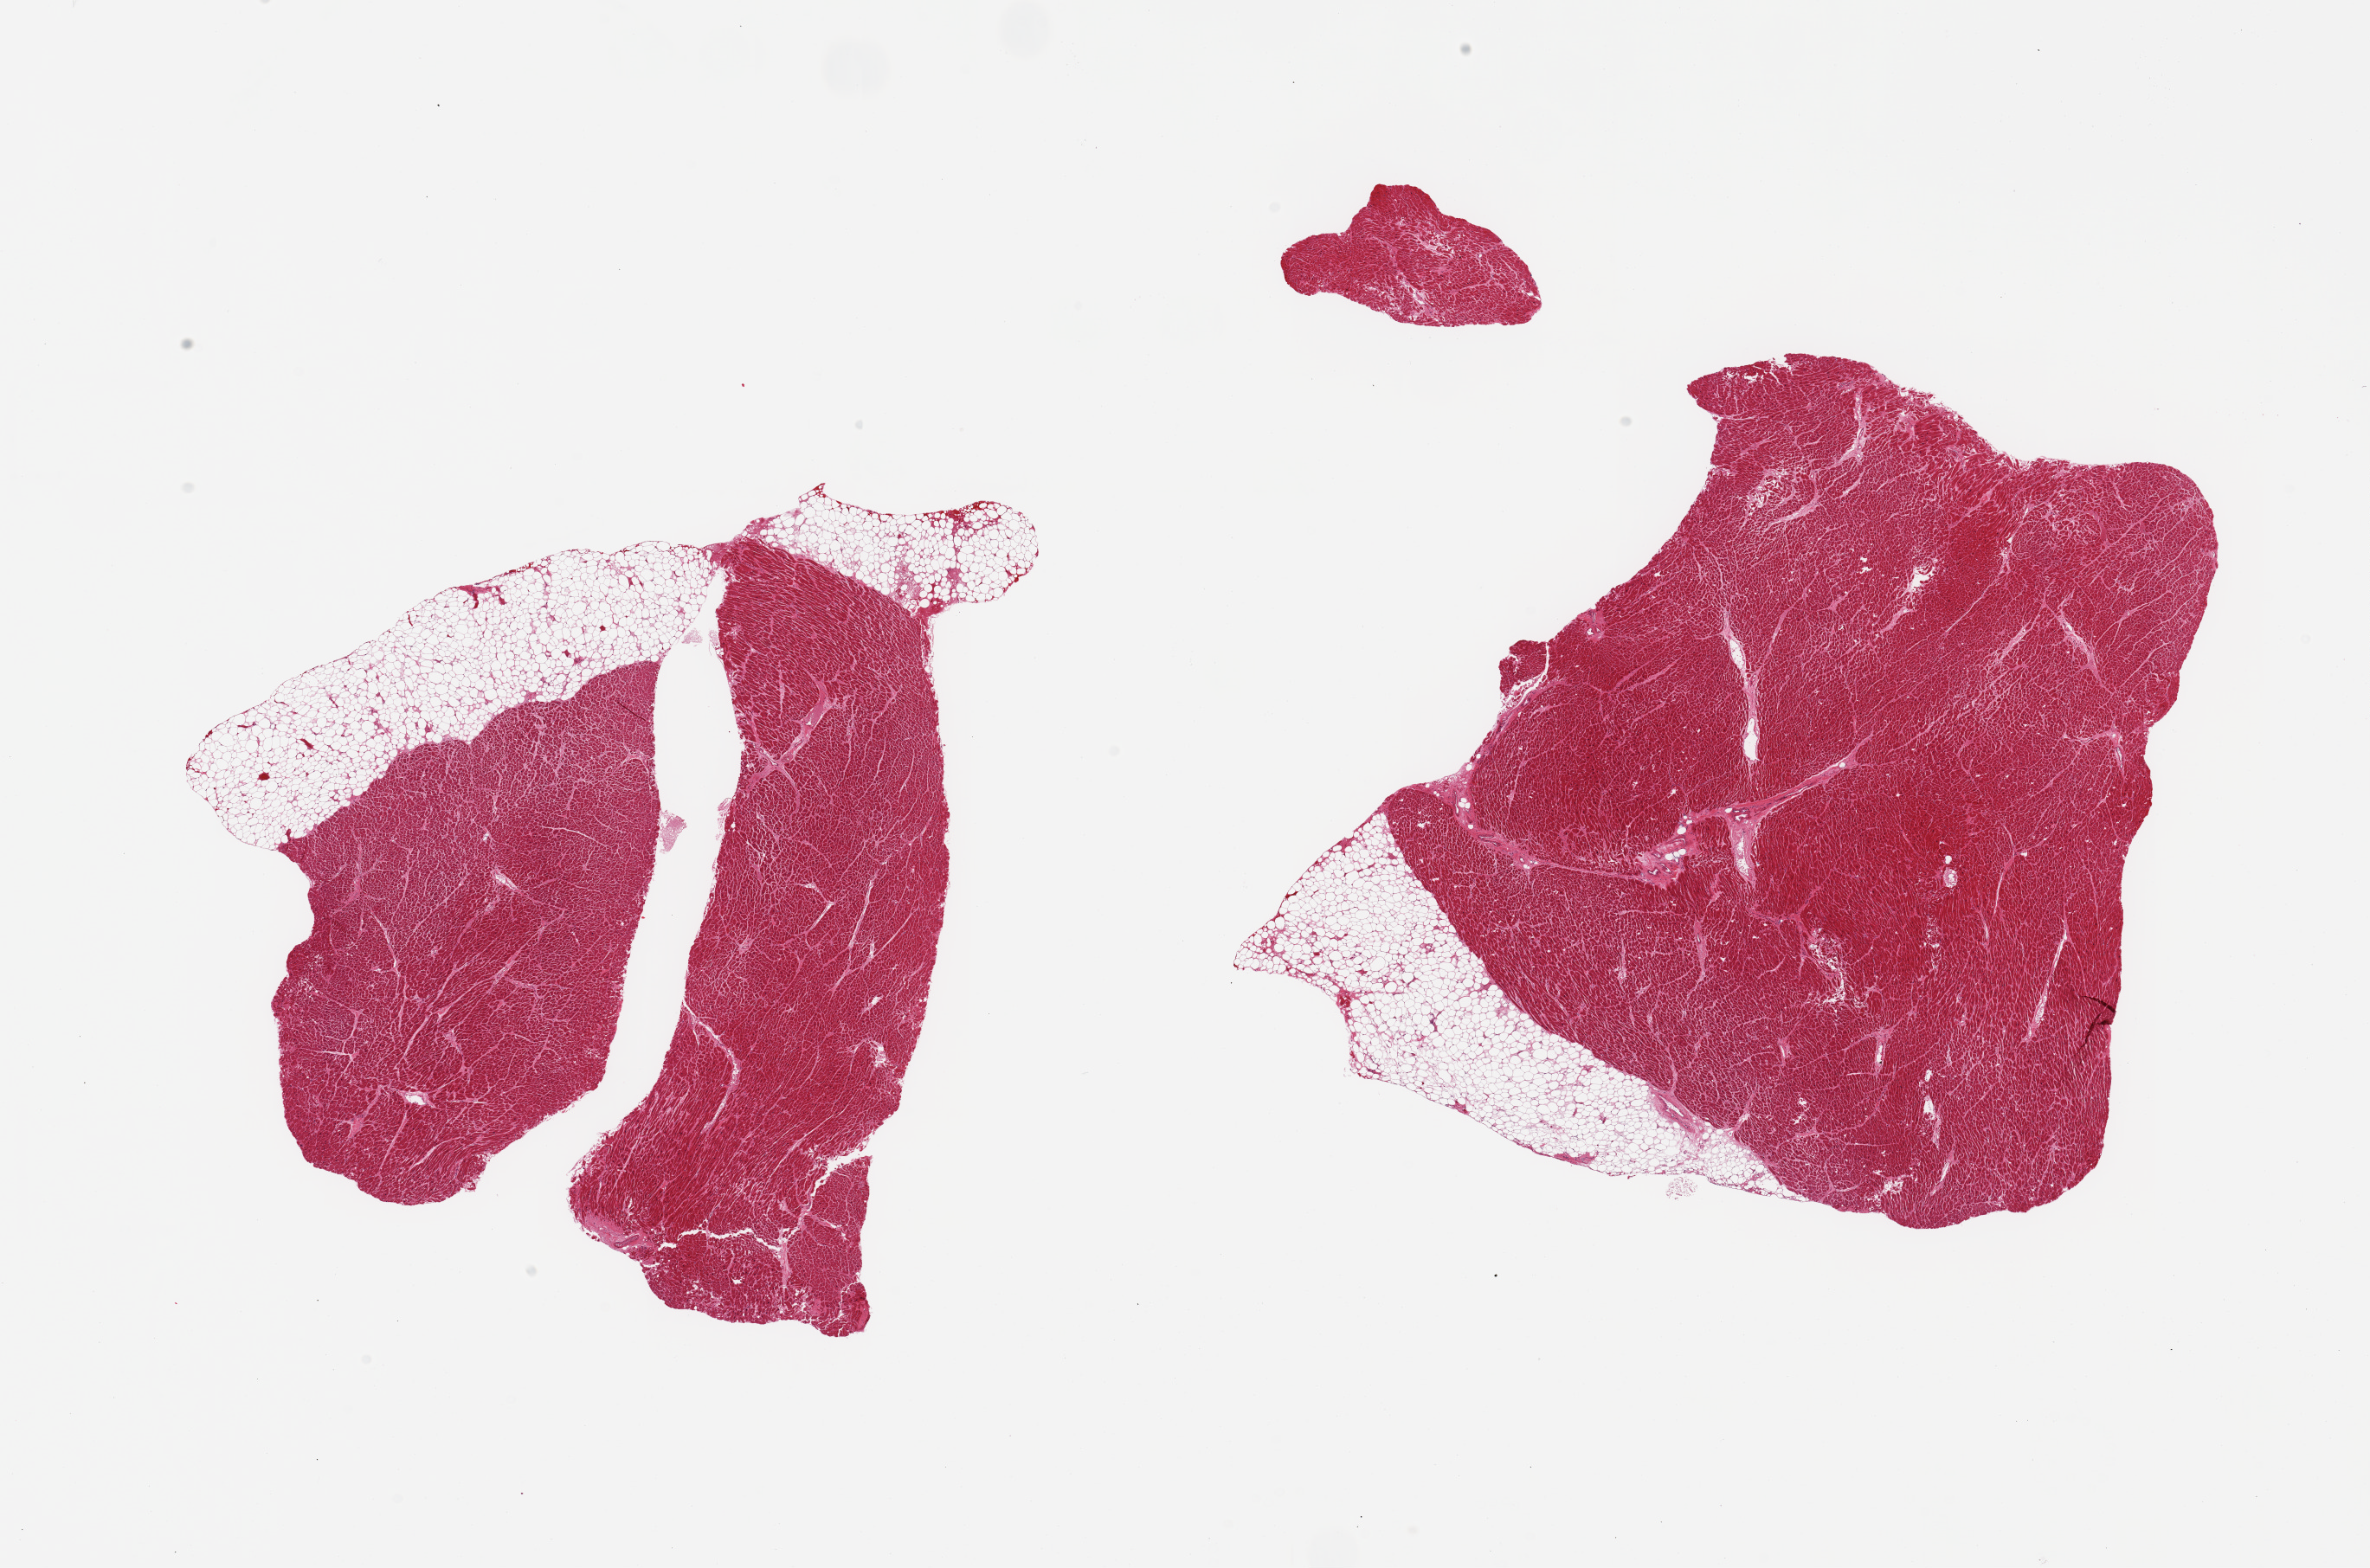
H&E whole-slide image, shown as a low-resolution overview of the whole scanned area (about 21.7 x 14.3 mm), PAXgene-fixed, paraffin-embedded tissue, section of heart (target tissue), donor tissue sample. Donor sex: male.
Pathologist's review note for this sample: 2 pieces; each piece has a thick external band of untrimmed fat along 1 edge, up to 1.9 mm thick occupying 40 % & 20% of aliquot.